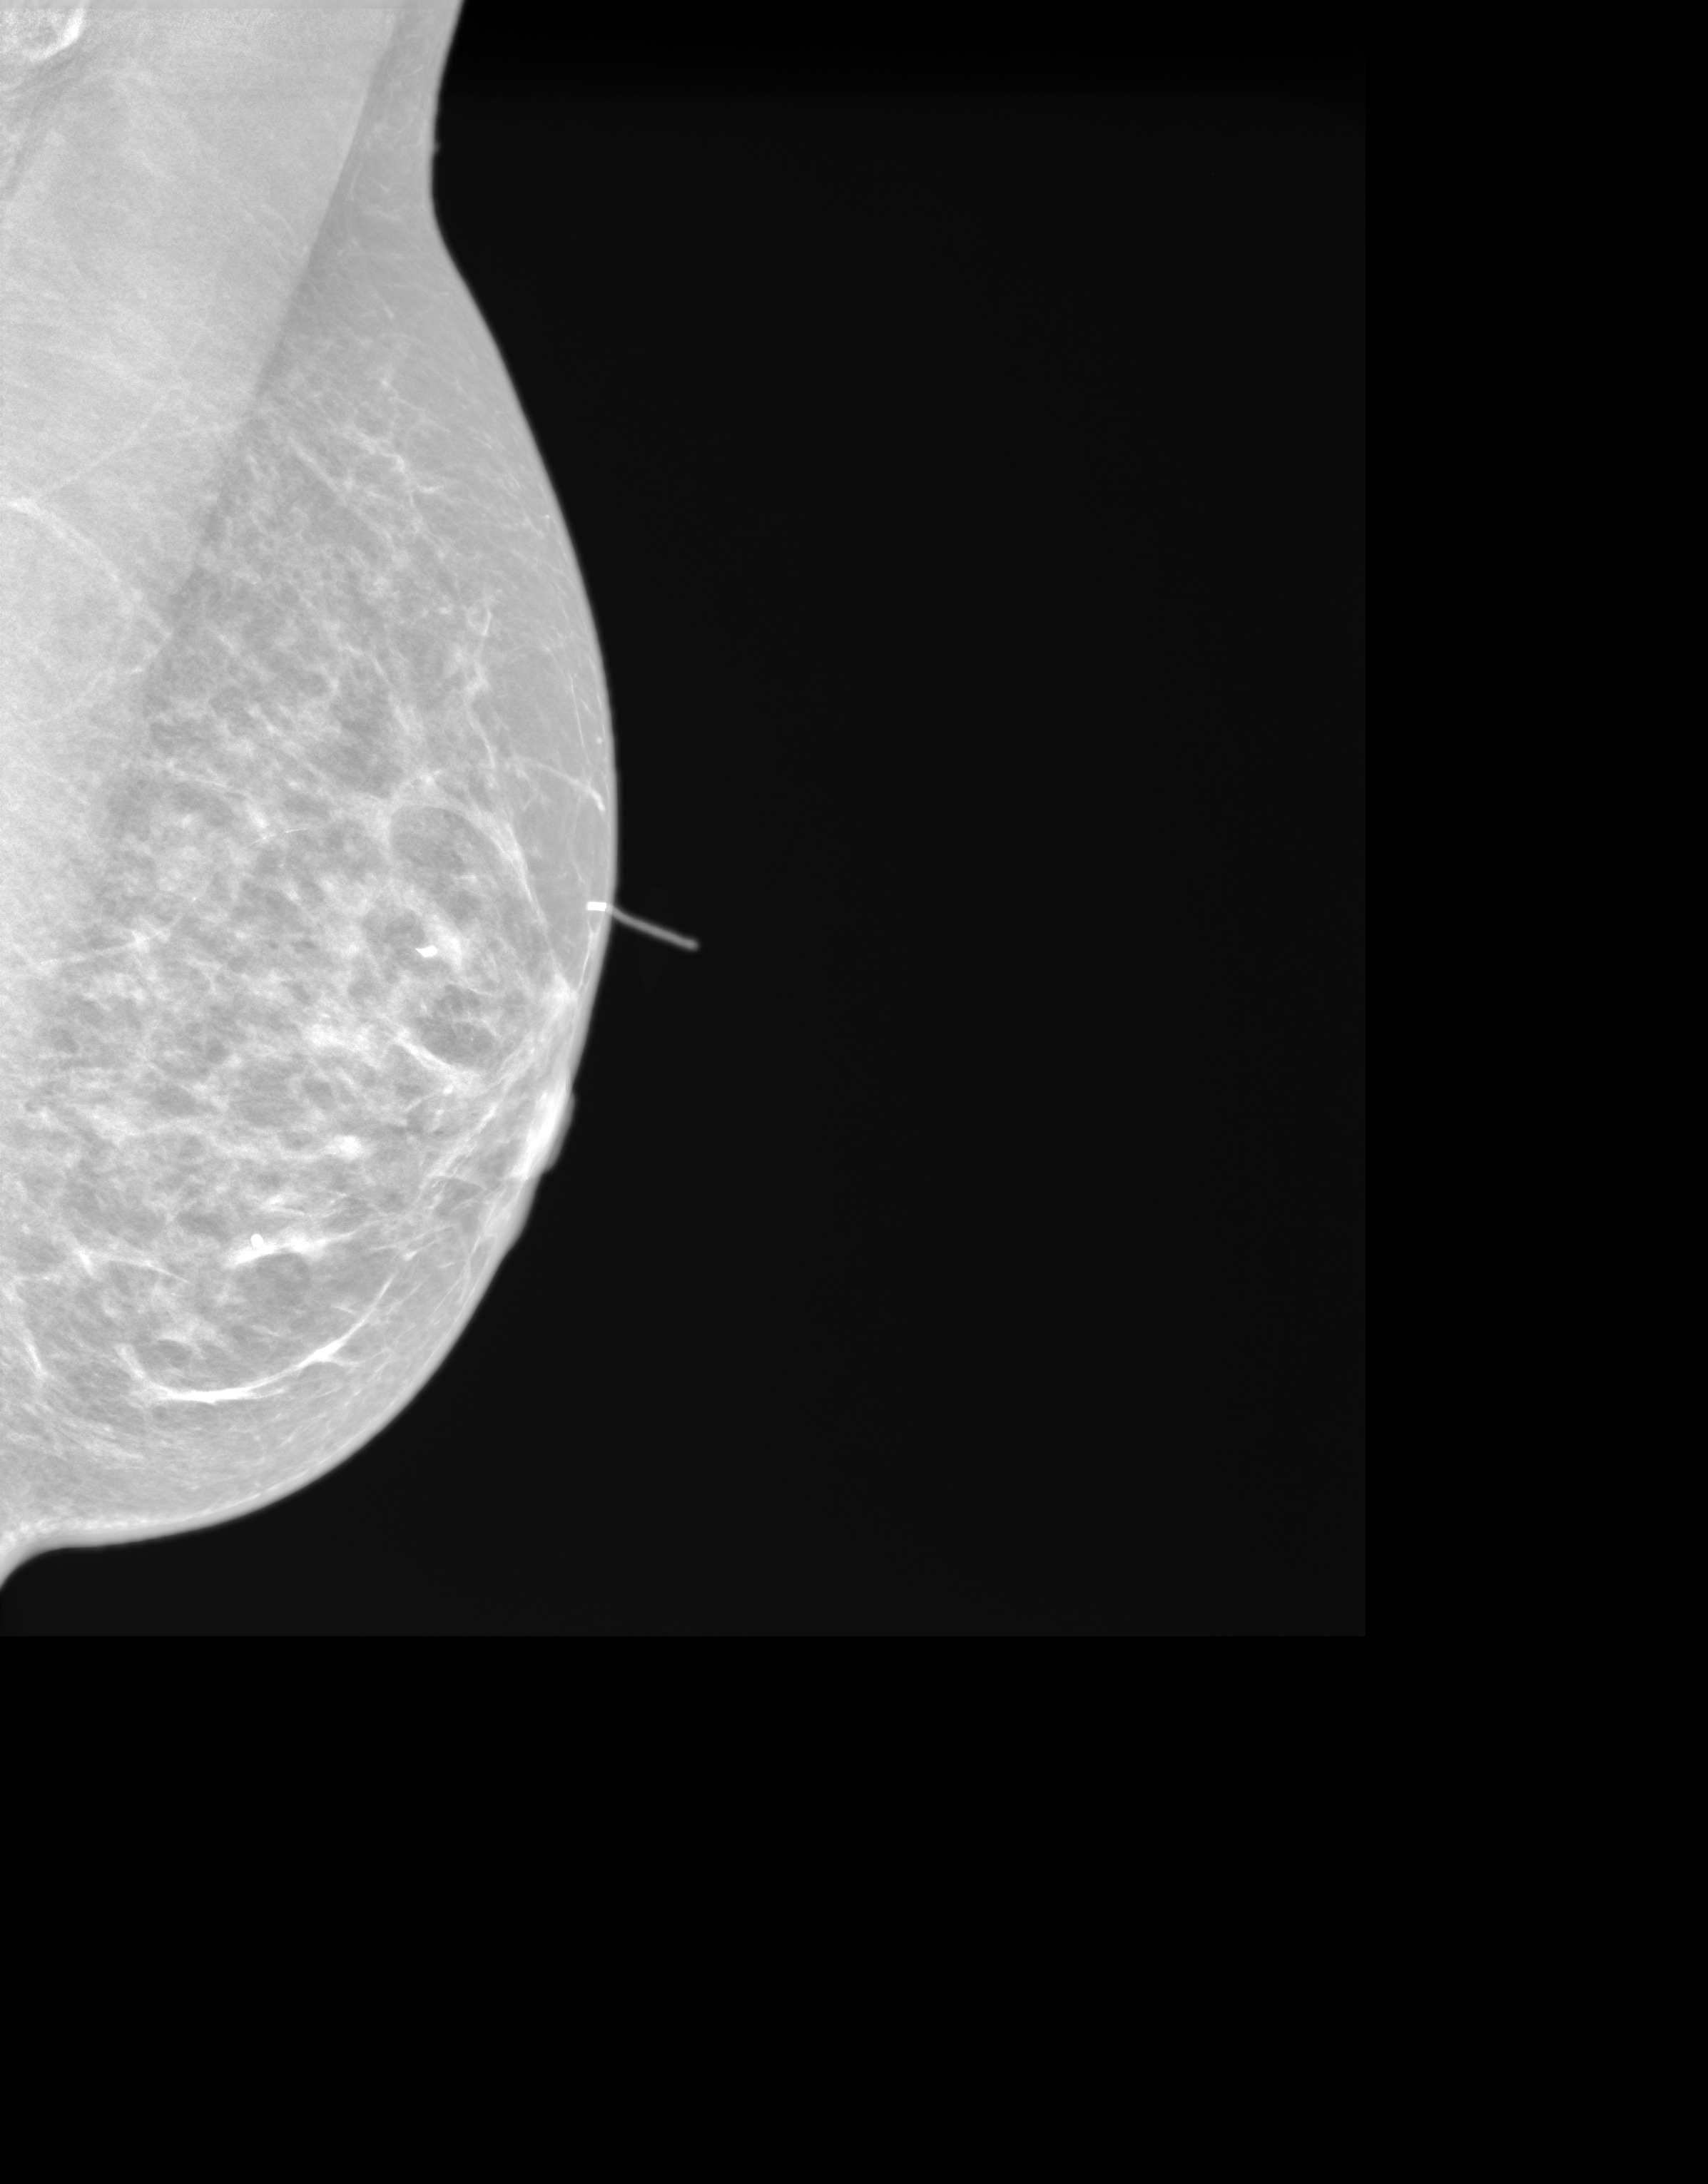
Synthesized 2-D mammogram reconstructed from digital breast tomosynthesis, left breast, medio-lateral oblique projection, annual screening mammography examination, system: SenoIris_1SP1.1(421). Patient: female, 69 years.
BI-RADS breast density category at the screening exam (both breasts, scale 1–4): 3. Final BI-RADS assessment for this screening round (tomosynthesis exam, both breasts): category 1. Recall: no recall after this screen.